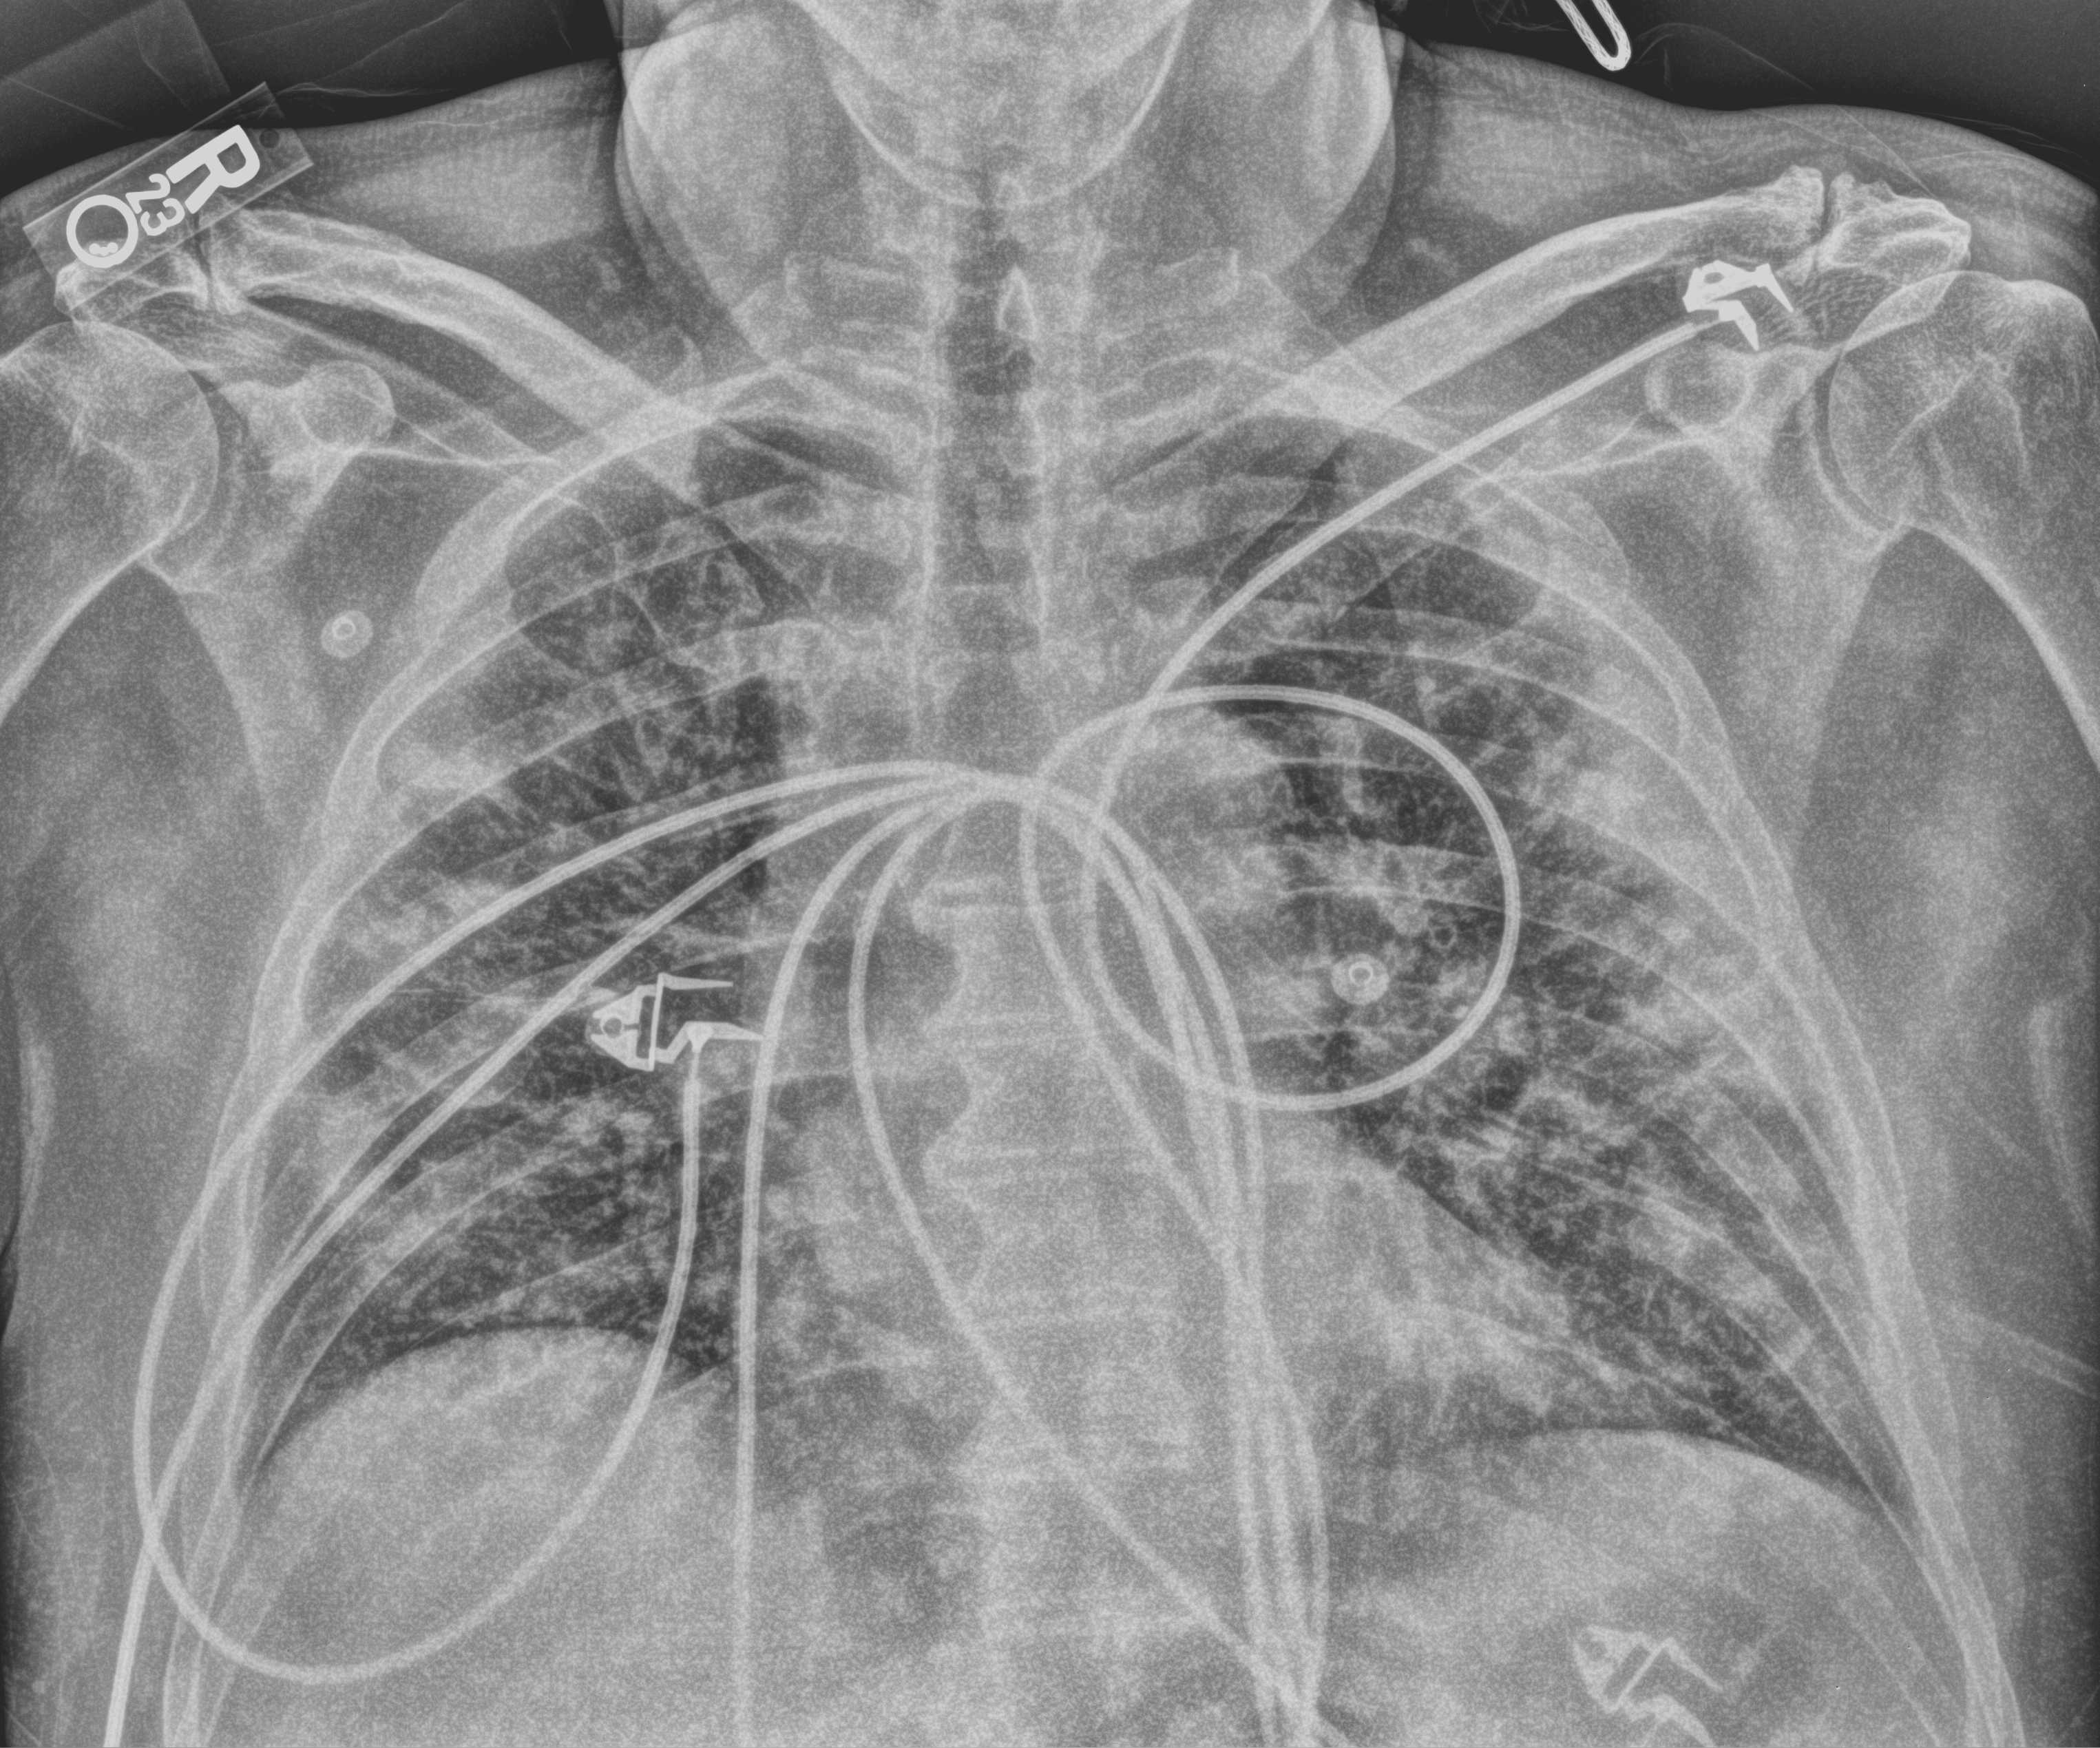
Chest X-ray (portable). Patient hospitalised with COVID-19; male, aged 60–74 years.
Hospital-stay facts (about this admission, not read from this image; timing relative to this image not recorded): smoking status (admission record): never; COPD (admission record): no.